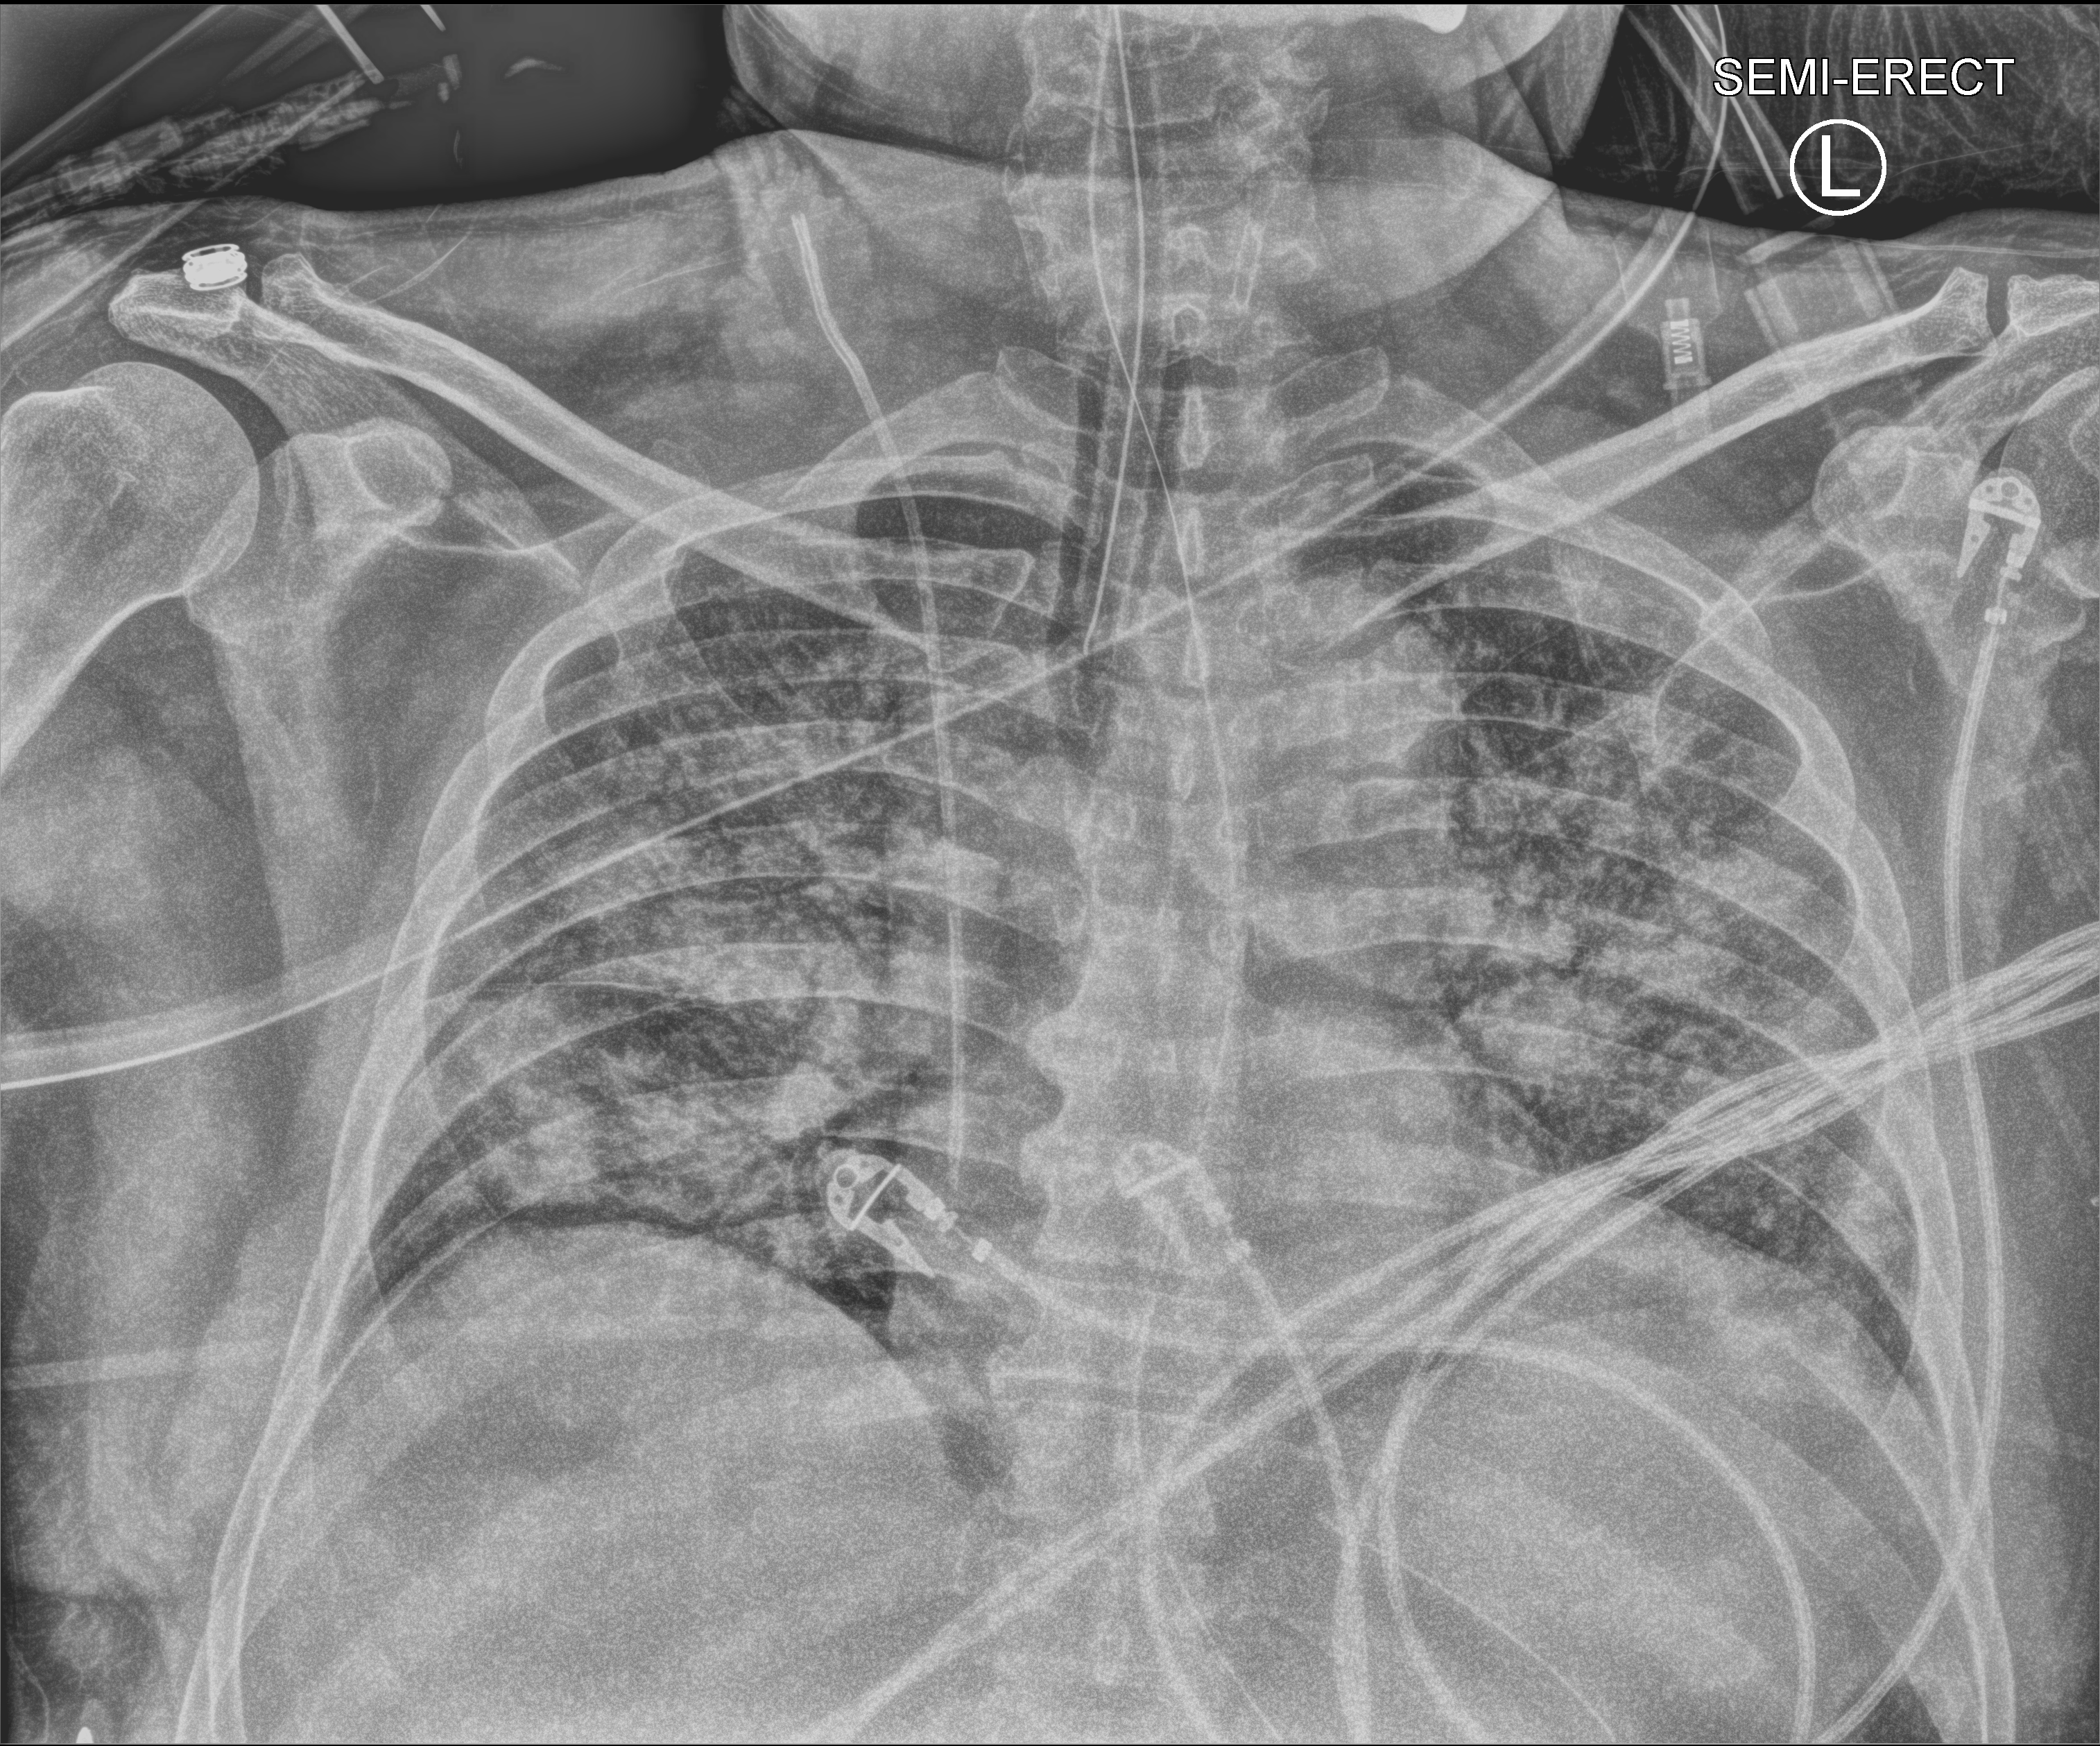
Portable chest radiograph; anteroposterior (AP) projection. Male patient hospitalised with COVID-19, age 60–74 years.
From the hospital-stay record, not from the radiograph (when in the stay this image was taken is not recorded): mechanically ventilated during this hospital stay: yes.